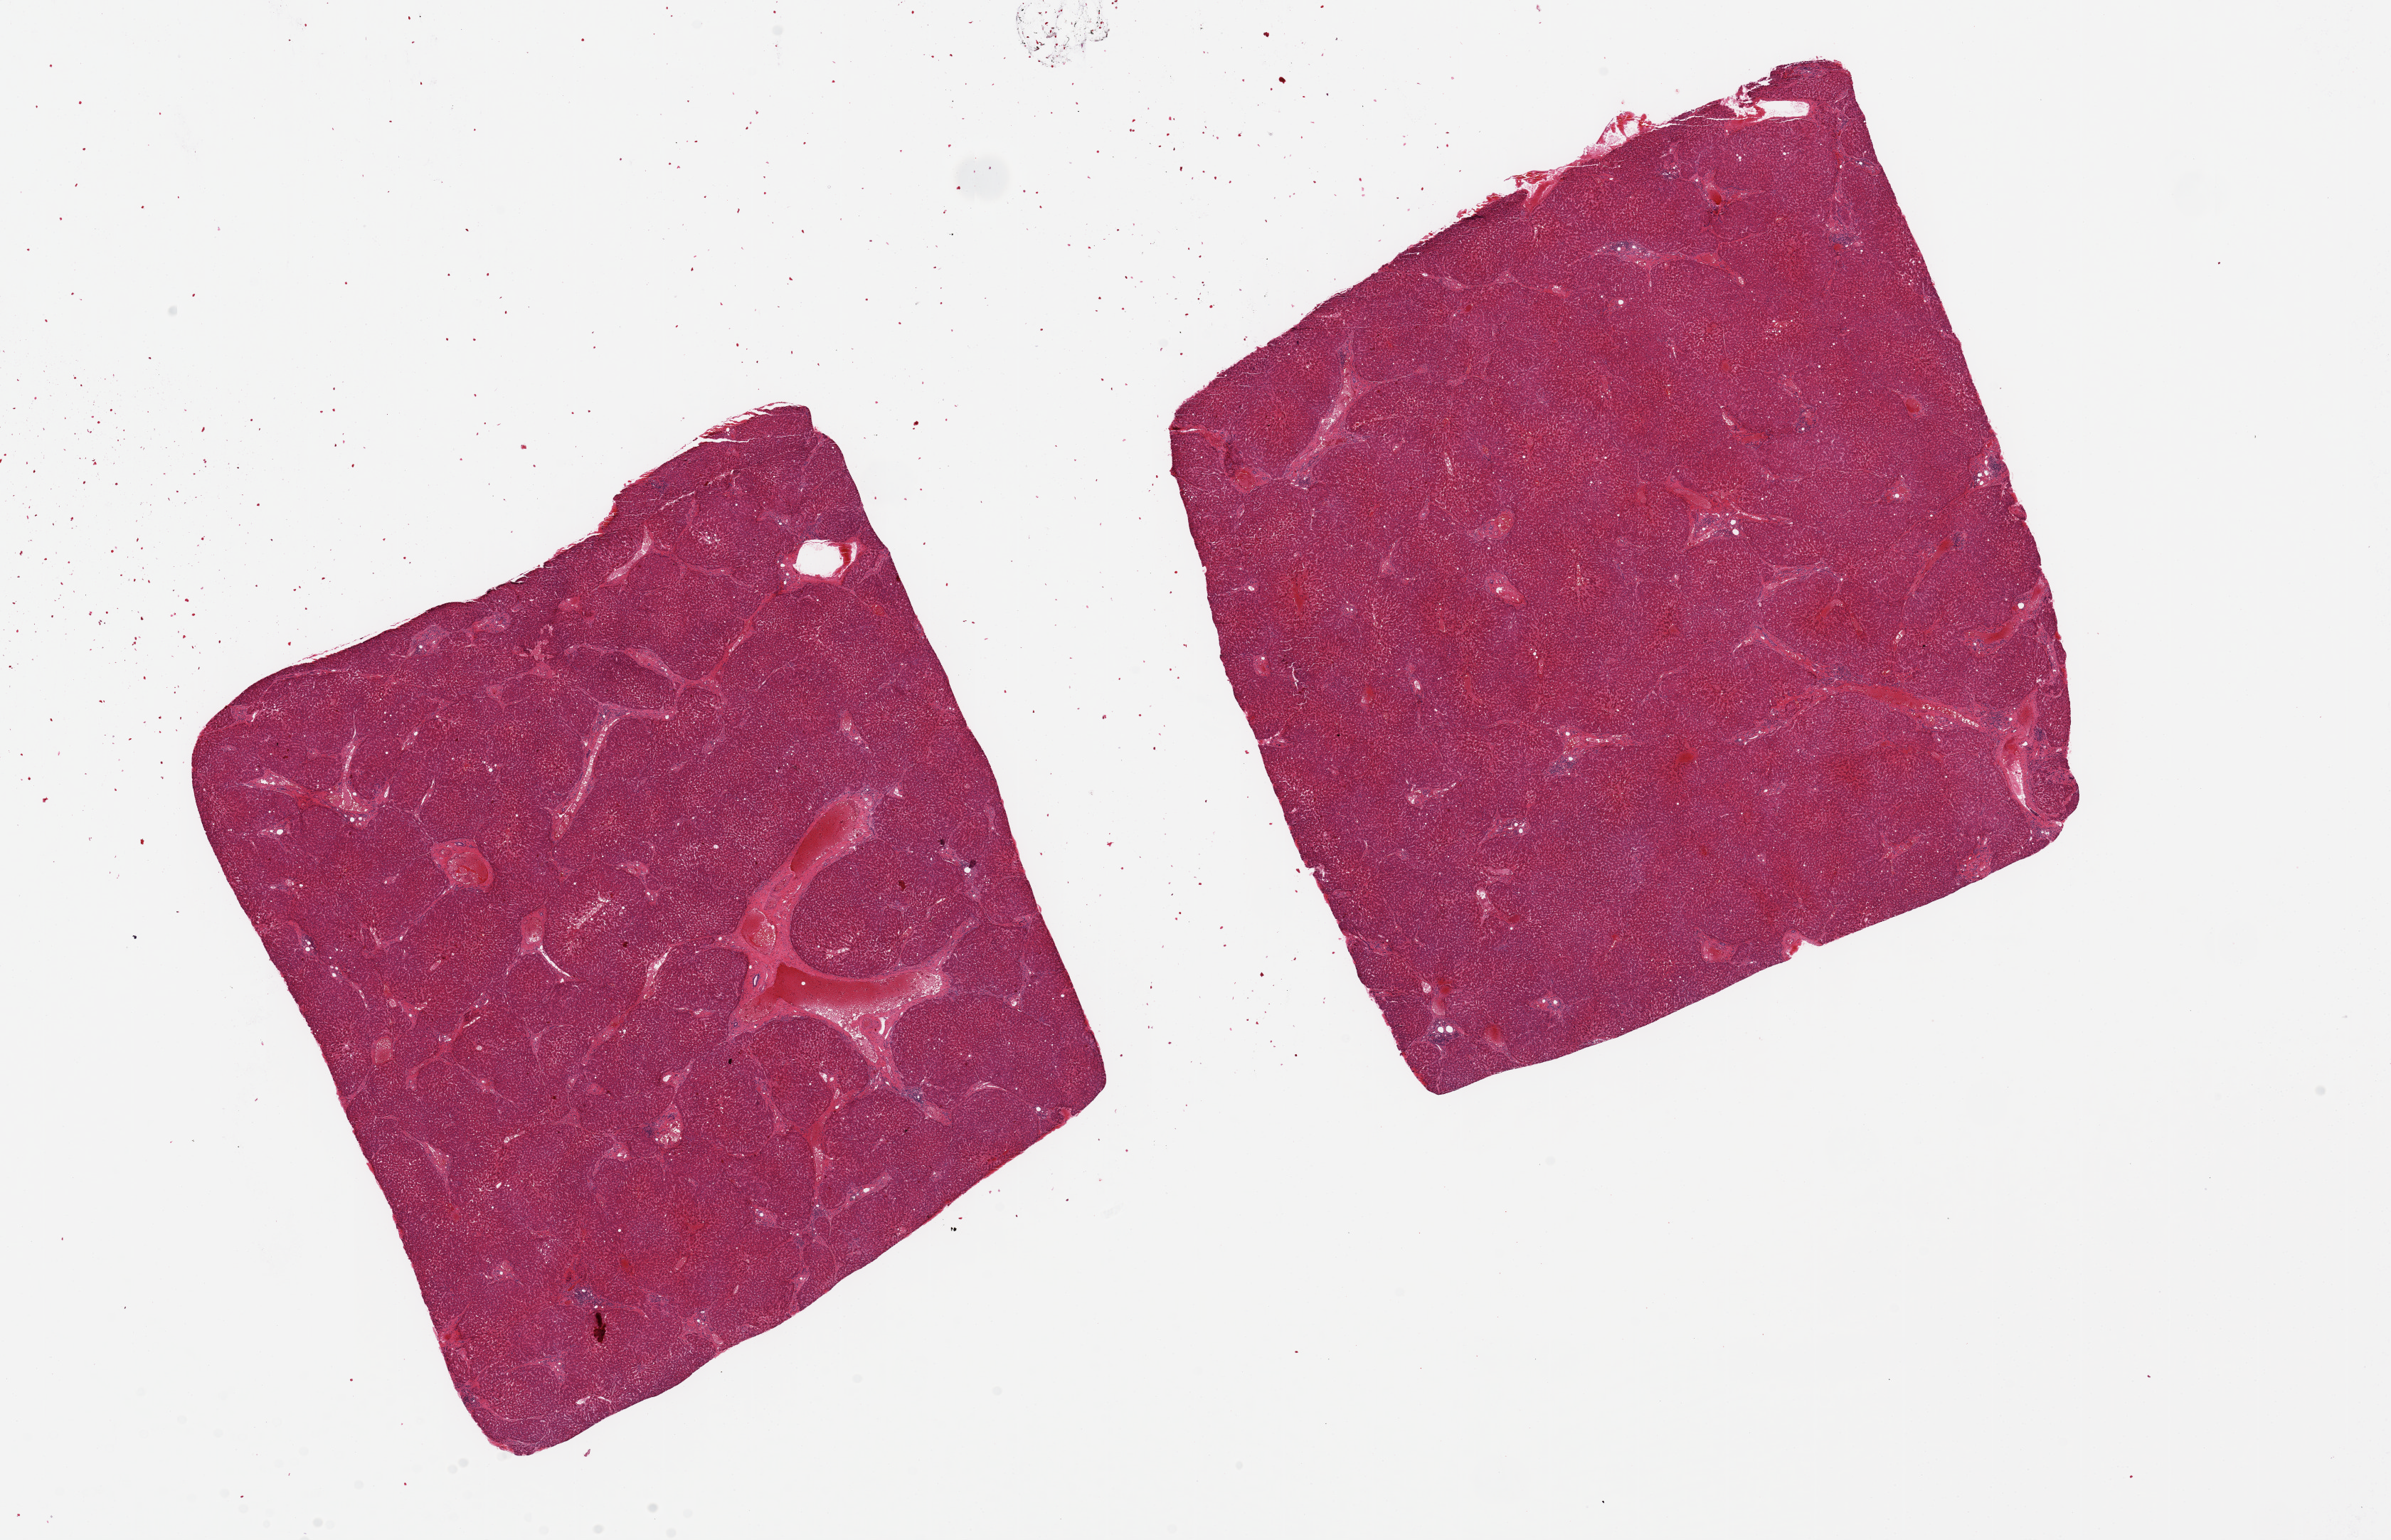
Whole-slide image, haematoxylin and eosin stain — shown as a low-resolution overview of the whole scanned area (about 26.6 x 17.1 mm, acquisition: 20x scan), PAXgene-fixed paraffin-embedded (PFPE) section, target tissue: liver, donor tissue sample. Donor: male.
Review note (as recorded): 2 pieces ~9x8mm. 10% macrovesicular steatosis.